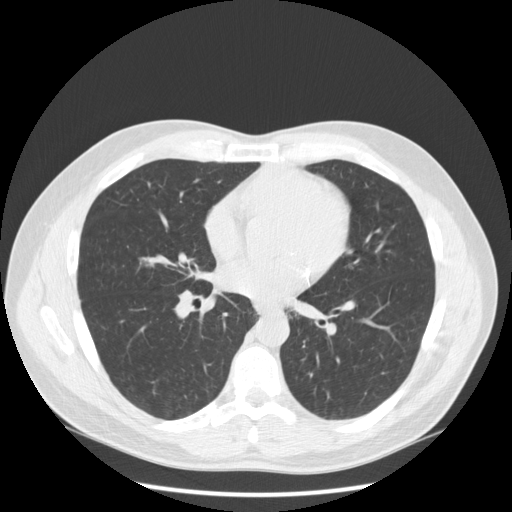
Low-dose screening chest CT, one axial slice; slice 104 of 234 in the series (ordered by position); reconstruction kernel STANDARD; lung window (W 1500 / L -600 HU); 512 × 512 image matrix, field of view 385 × 385 mm.
Structures marked on this image (outlined manually by an expert reader):
- lesion 1 (tumor, middle lobe of right lung): bounding box <138,257,155,267> (left, top, right, bottom; pixels)